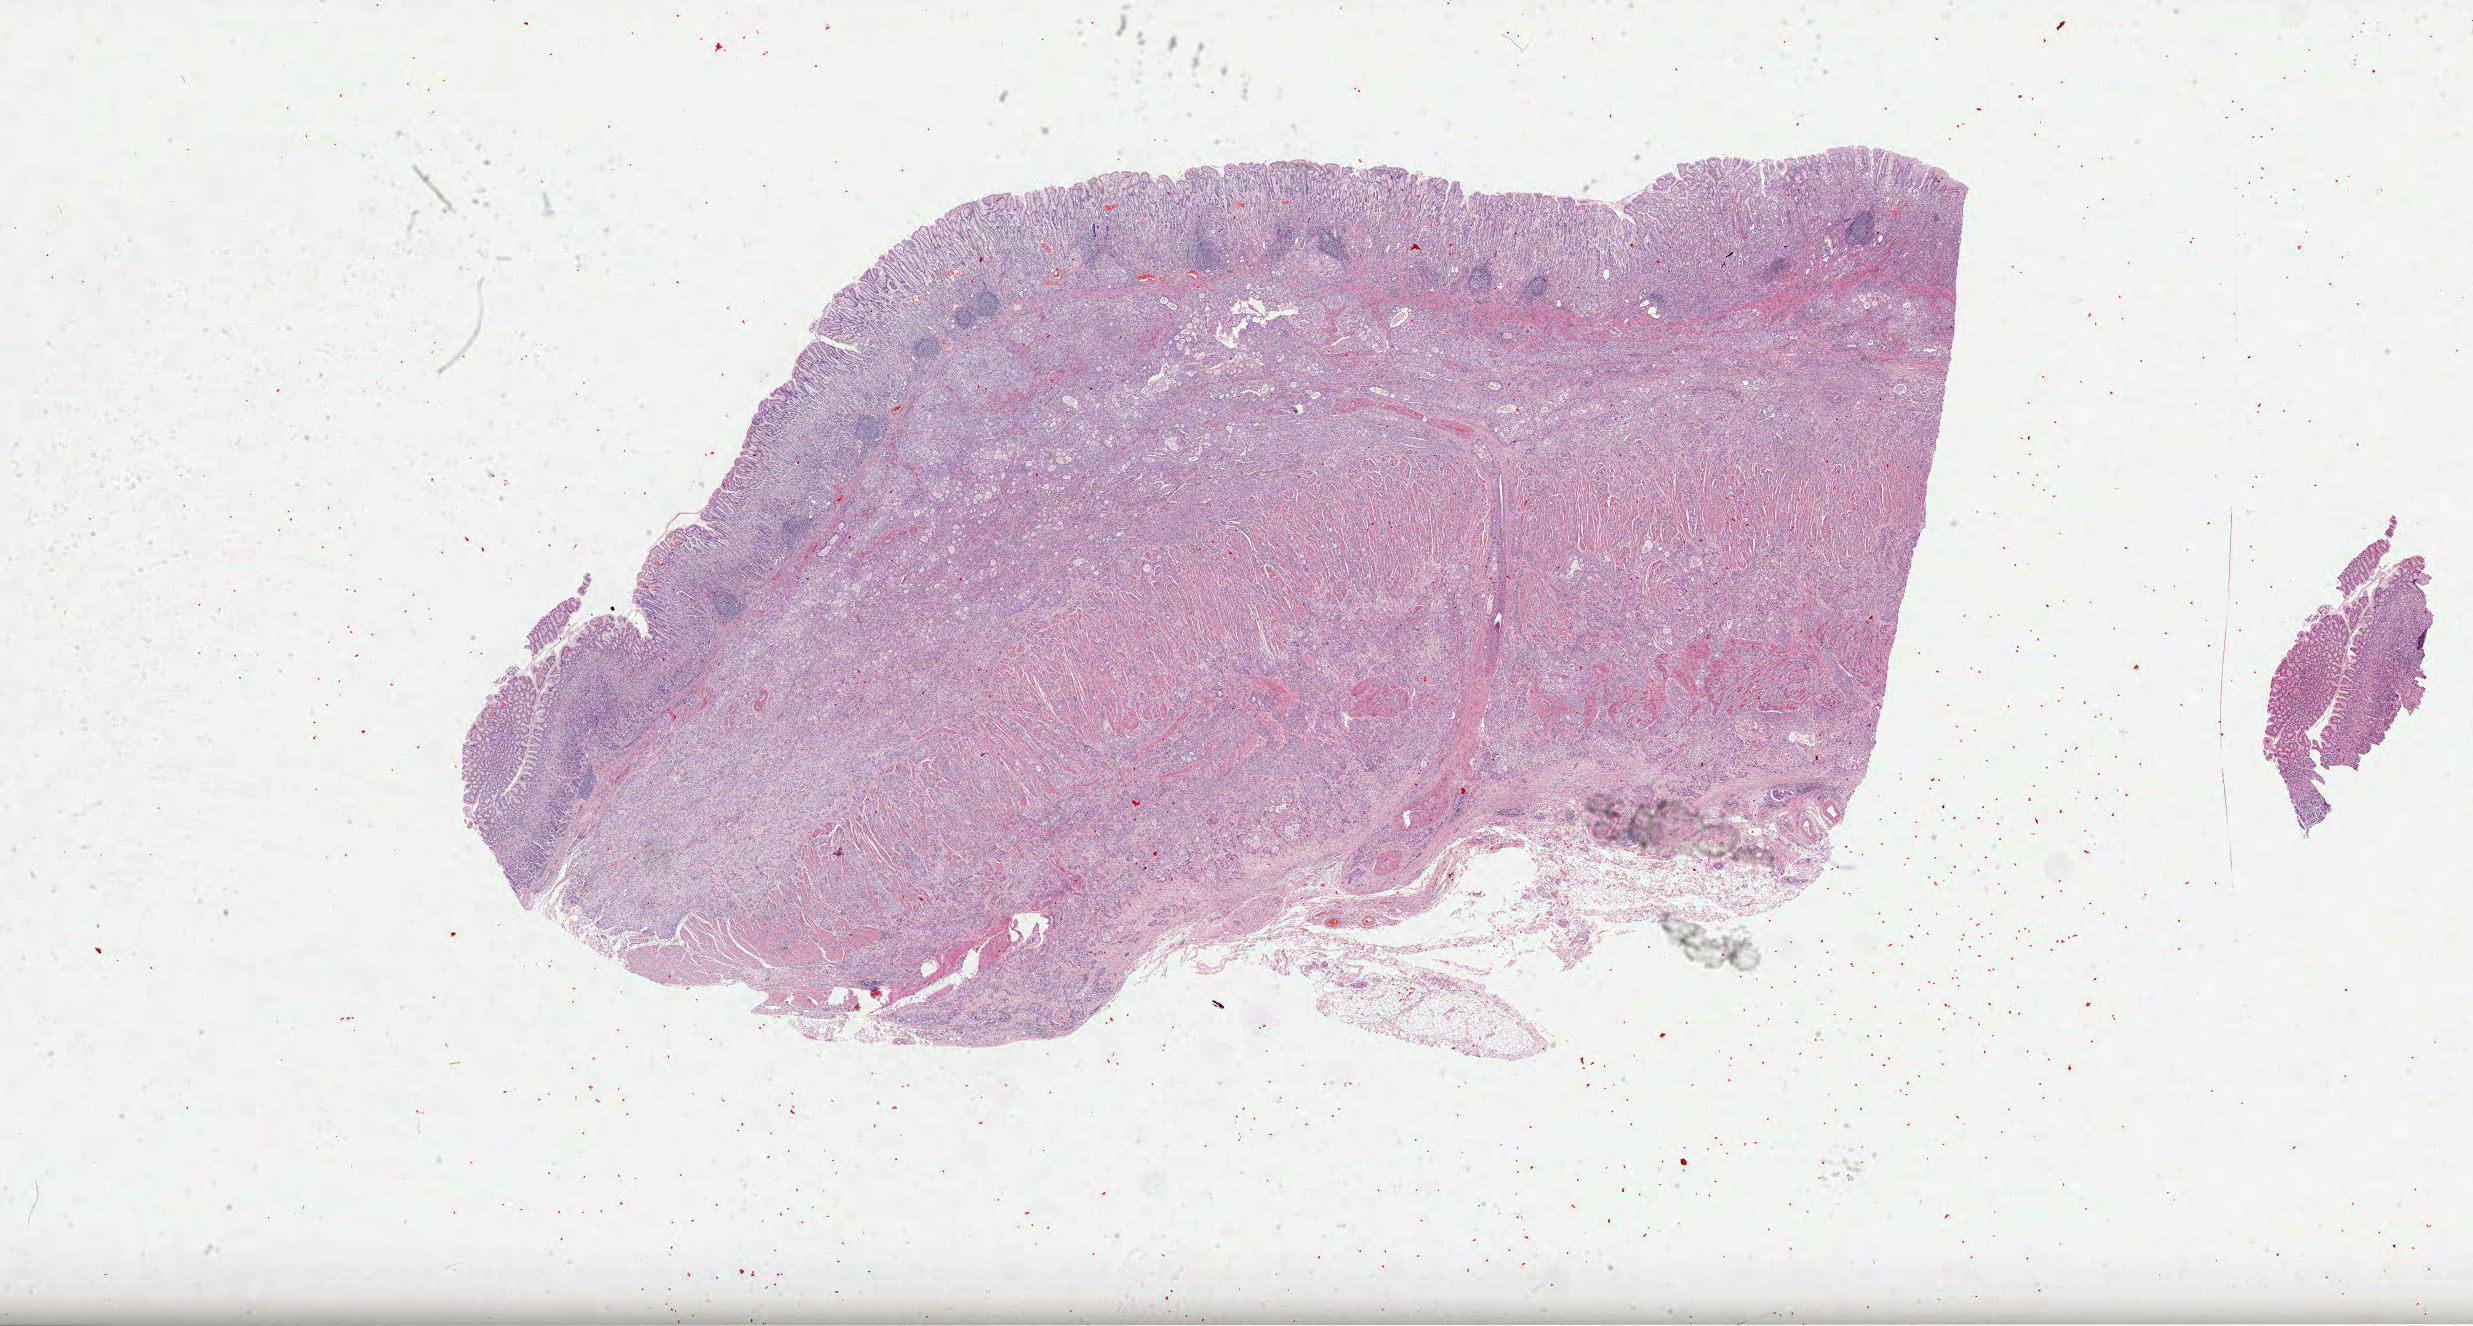
Digitized Hematoxylin and eosin (H&E) stained tissue section (whole slide), shown as a low-resolution overview of the whole scanned area (about 39.9 x 21.4 mm, acquisition: 40x scan), formalin-fixed paraffin-embedded (FFPE) diagnostic section, sample: primary tumour, stomach. Patient: female, age at initial diagnosis 64 years. Histologic grade: G3 (poorly differentiated).
- diagnosis: Carcinoma, diffuse type (cardia, NOS)
- lymph nodes positive (case pathology): 2 of 16 examined